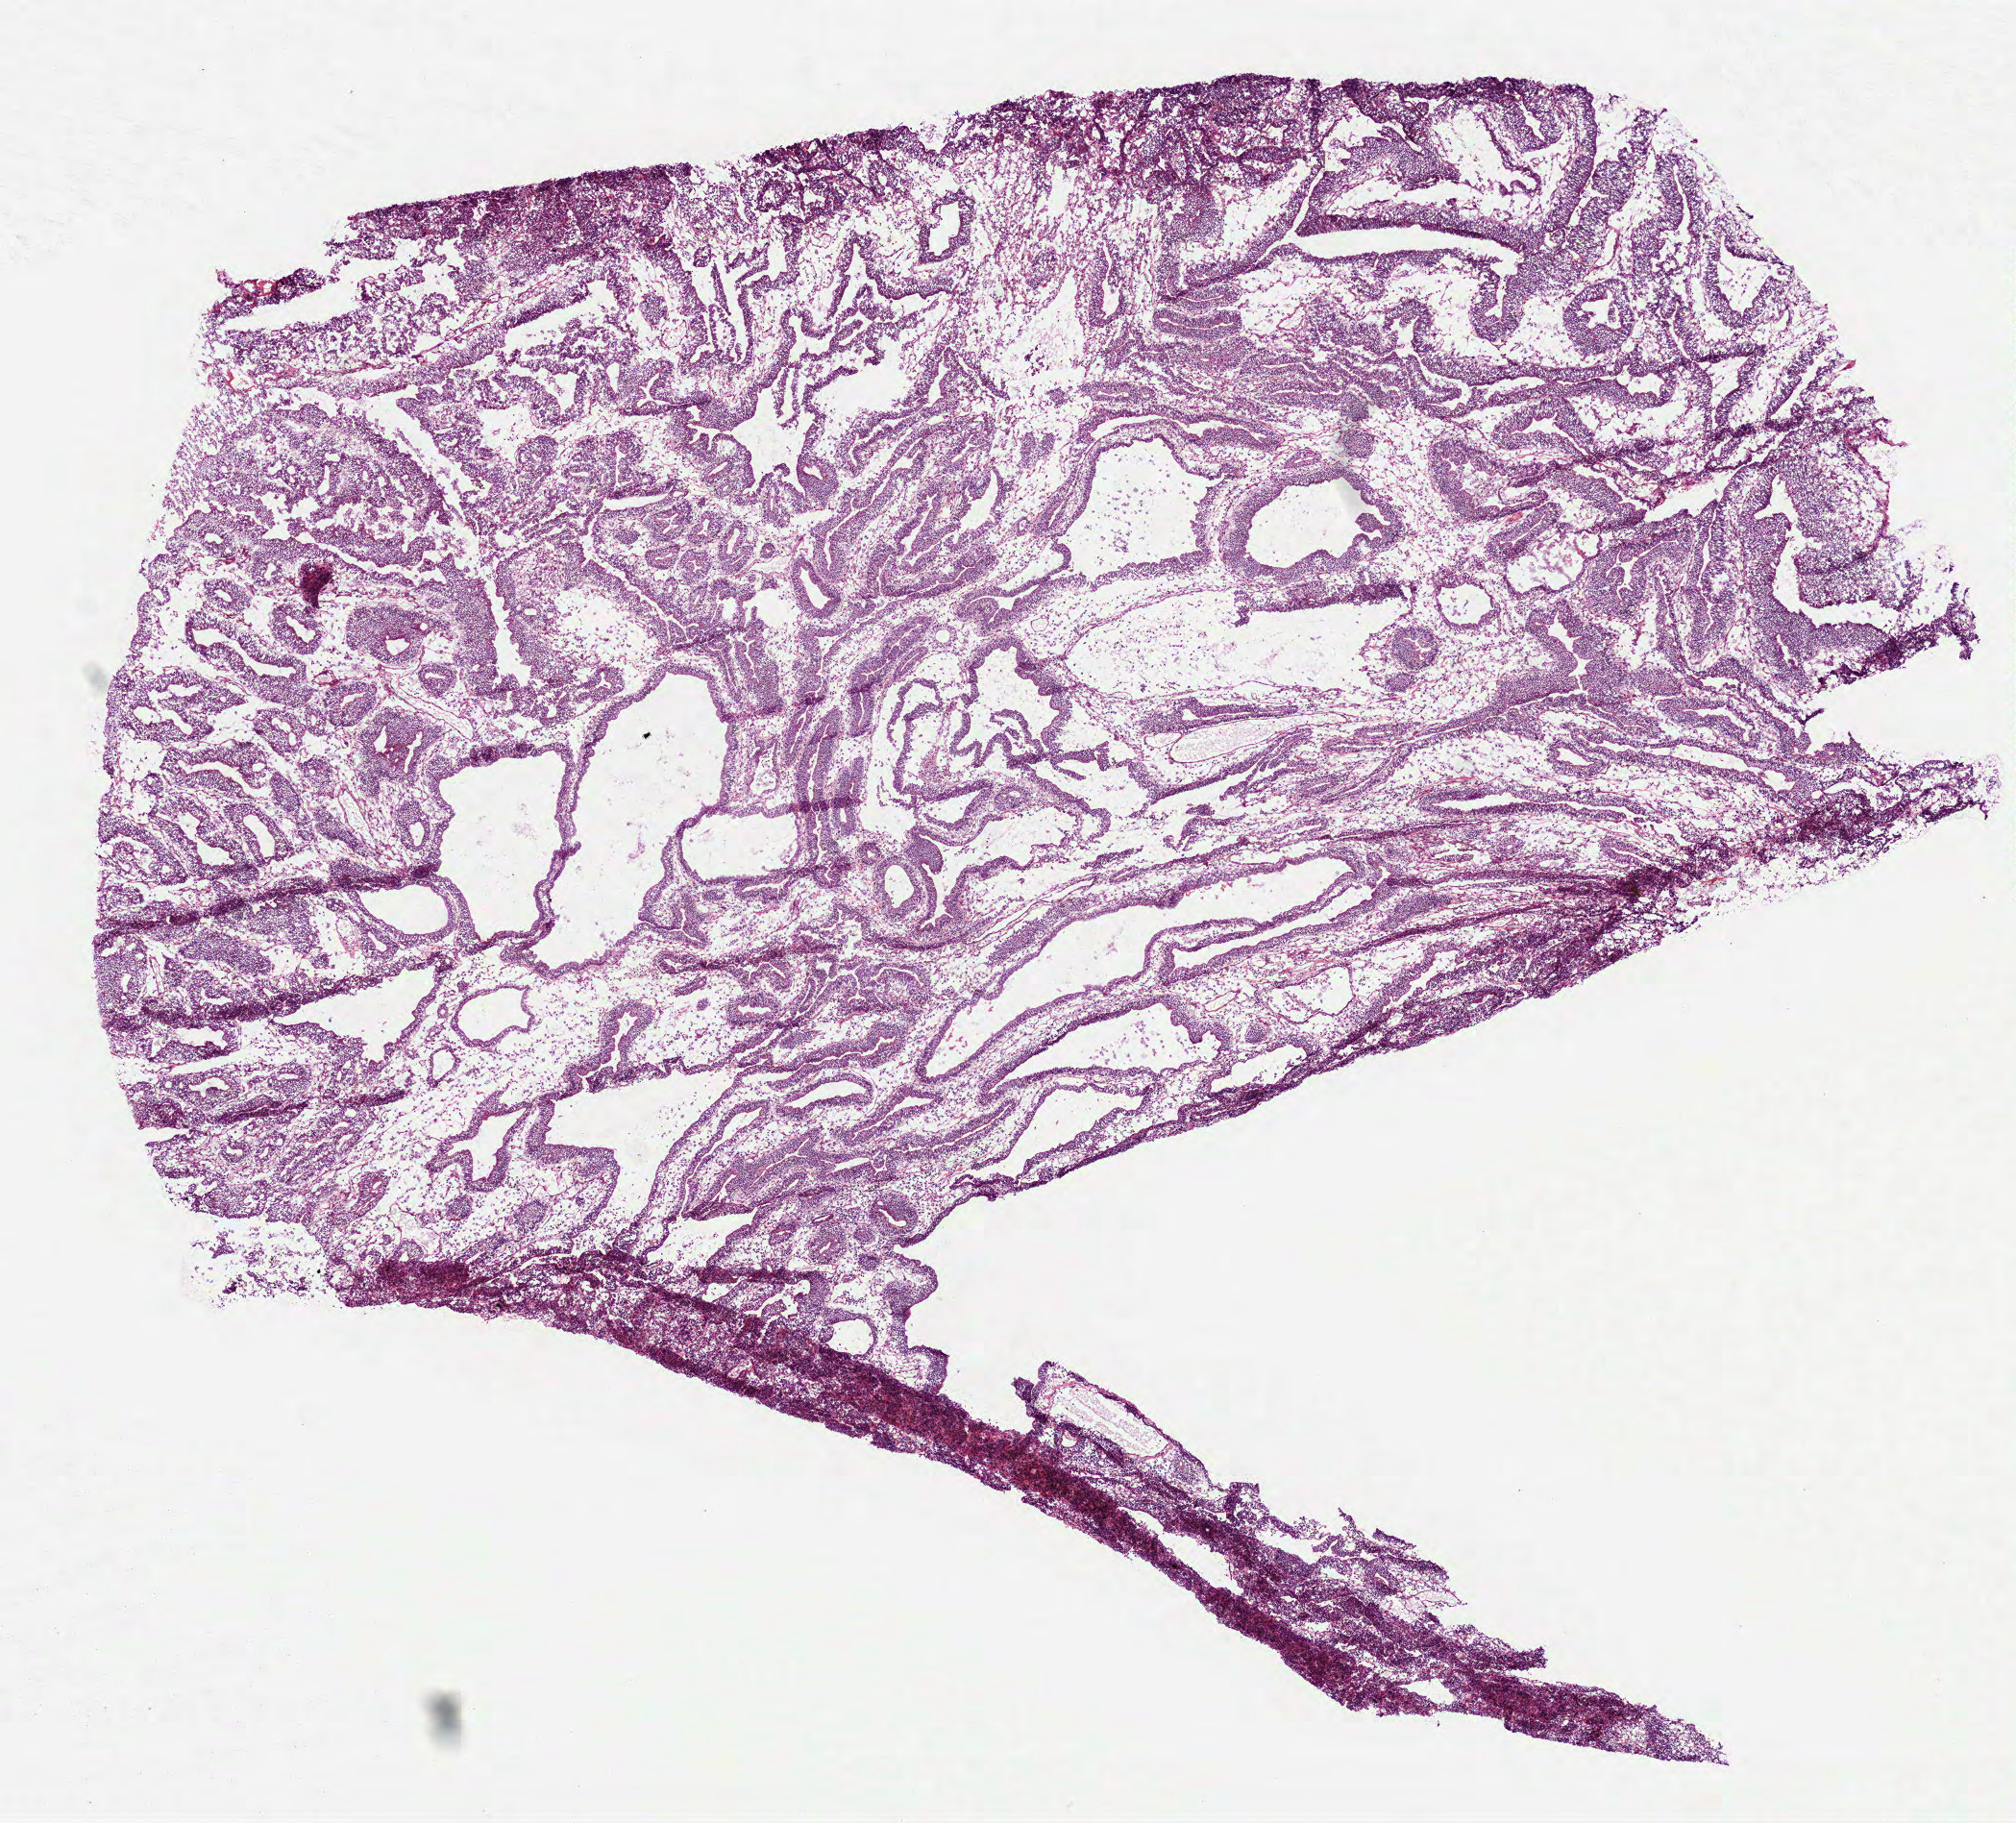
H&E whole-slide image, low-resolution overview of the scanned area, about 8.5 x 7.6 mm; frozen section from the top of the tissue portion; sample: primary tumour, stomach. Male patient. Histologic grade: G2 (moderately differentiated). Composition of this section per pathologist review: tumour cells 100%, tumour nuclei 80%, normal cells 0%, stromal cells 0%, necrosis 0%. Inflammatory infiltration, as recorded: lymphocyte infiltration 5%, monocyte infiltration 5%, neutrophil infiltration 5%.
* AJCC pathologic stage: IA
* histologic diagnosis: Adenocarcinoma, intestinal type (body of stomach)
* TNM: T1 N0 M0